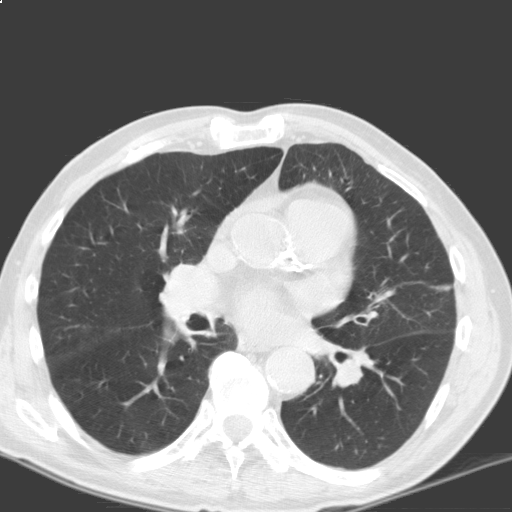
Axial slice from a low-dose chest CT screening exam; baseline annual screen; lung window (W 1500 / L -600 HU); 3.2 mm slice thickness; slice 89 of 184 in the series; 512 × 512 image matrix, field of view 318 × 318 mm. Male, age 69 years at enrolment. Current smoker at enrolment.
Expert reader's lesion annotation, bounding box <151,196,206,252> (left, top, right, bottom; pixels). The exam's reader record, not a measurement of the box and not confirmed to be the same lesion: non-calcified nodule or mass ≥4 mm, left lower lobe, 5 × 5 mm, smooth margins, soft tissue attenuation. Note: the box lies in the patient's right hemithorax on this image, whereas the reader's record names the left lung; they may be different findings. Official screen result: positive, change unspecified: nodule(s) >= 4 mm or enlarging nodule(s), mass(es), or other non-specific abnormalities suspicious for lung cancer. Participant outcome: lung cancer diagnosed 317 days after this screen — squamous cell carcinoma, NOS, right upper lobe, moderately differentiated (G2), stage IB (AJCC 6th edition), 40 mm at pathology.